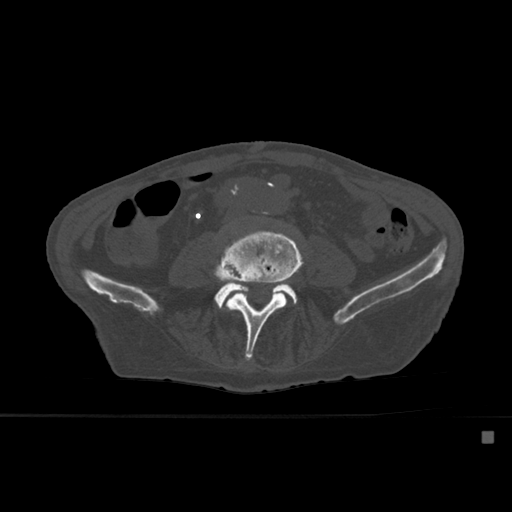
CT including the spine, one axial slice; position 190 of 527 along the scan axis; bone window (W 1800 / L 400 HU); 1.5 mm slice thickness; 512 × 512 image matrix. Patient: male, 78 years. From the clinical record (not read from this slice): primary cancer: prostate.
Structures marked on this image (semi-automatic segmentation, software-assisted and operator-edited):
- L4 vertebra: bounding box <213,229,303,361> (left, top, right, bottom; pixels)
- L5 vertebra: <193,283,298,308>